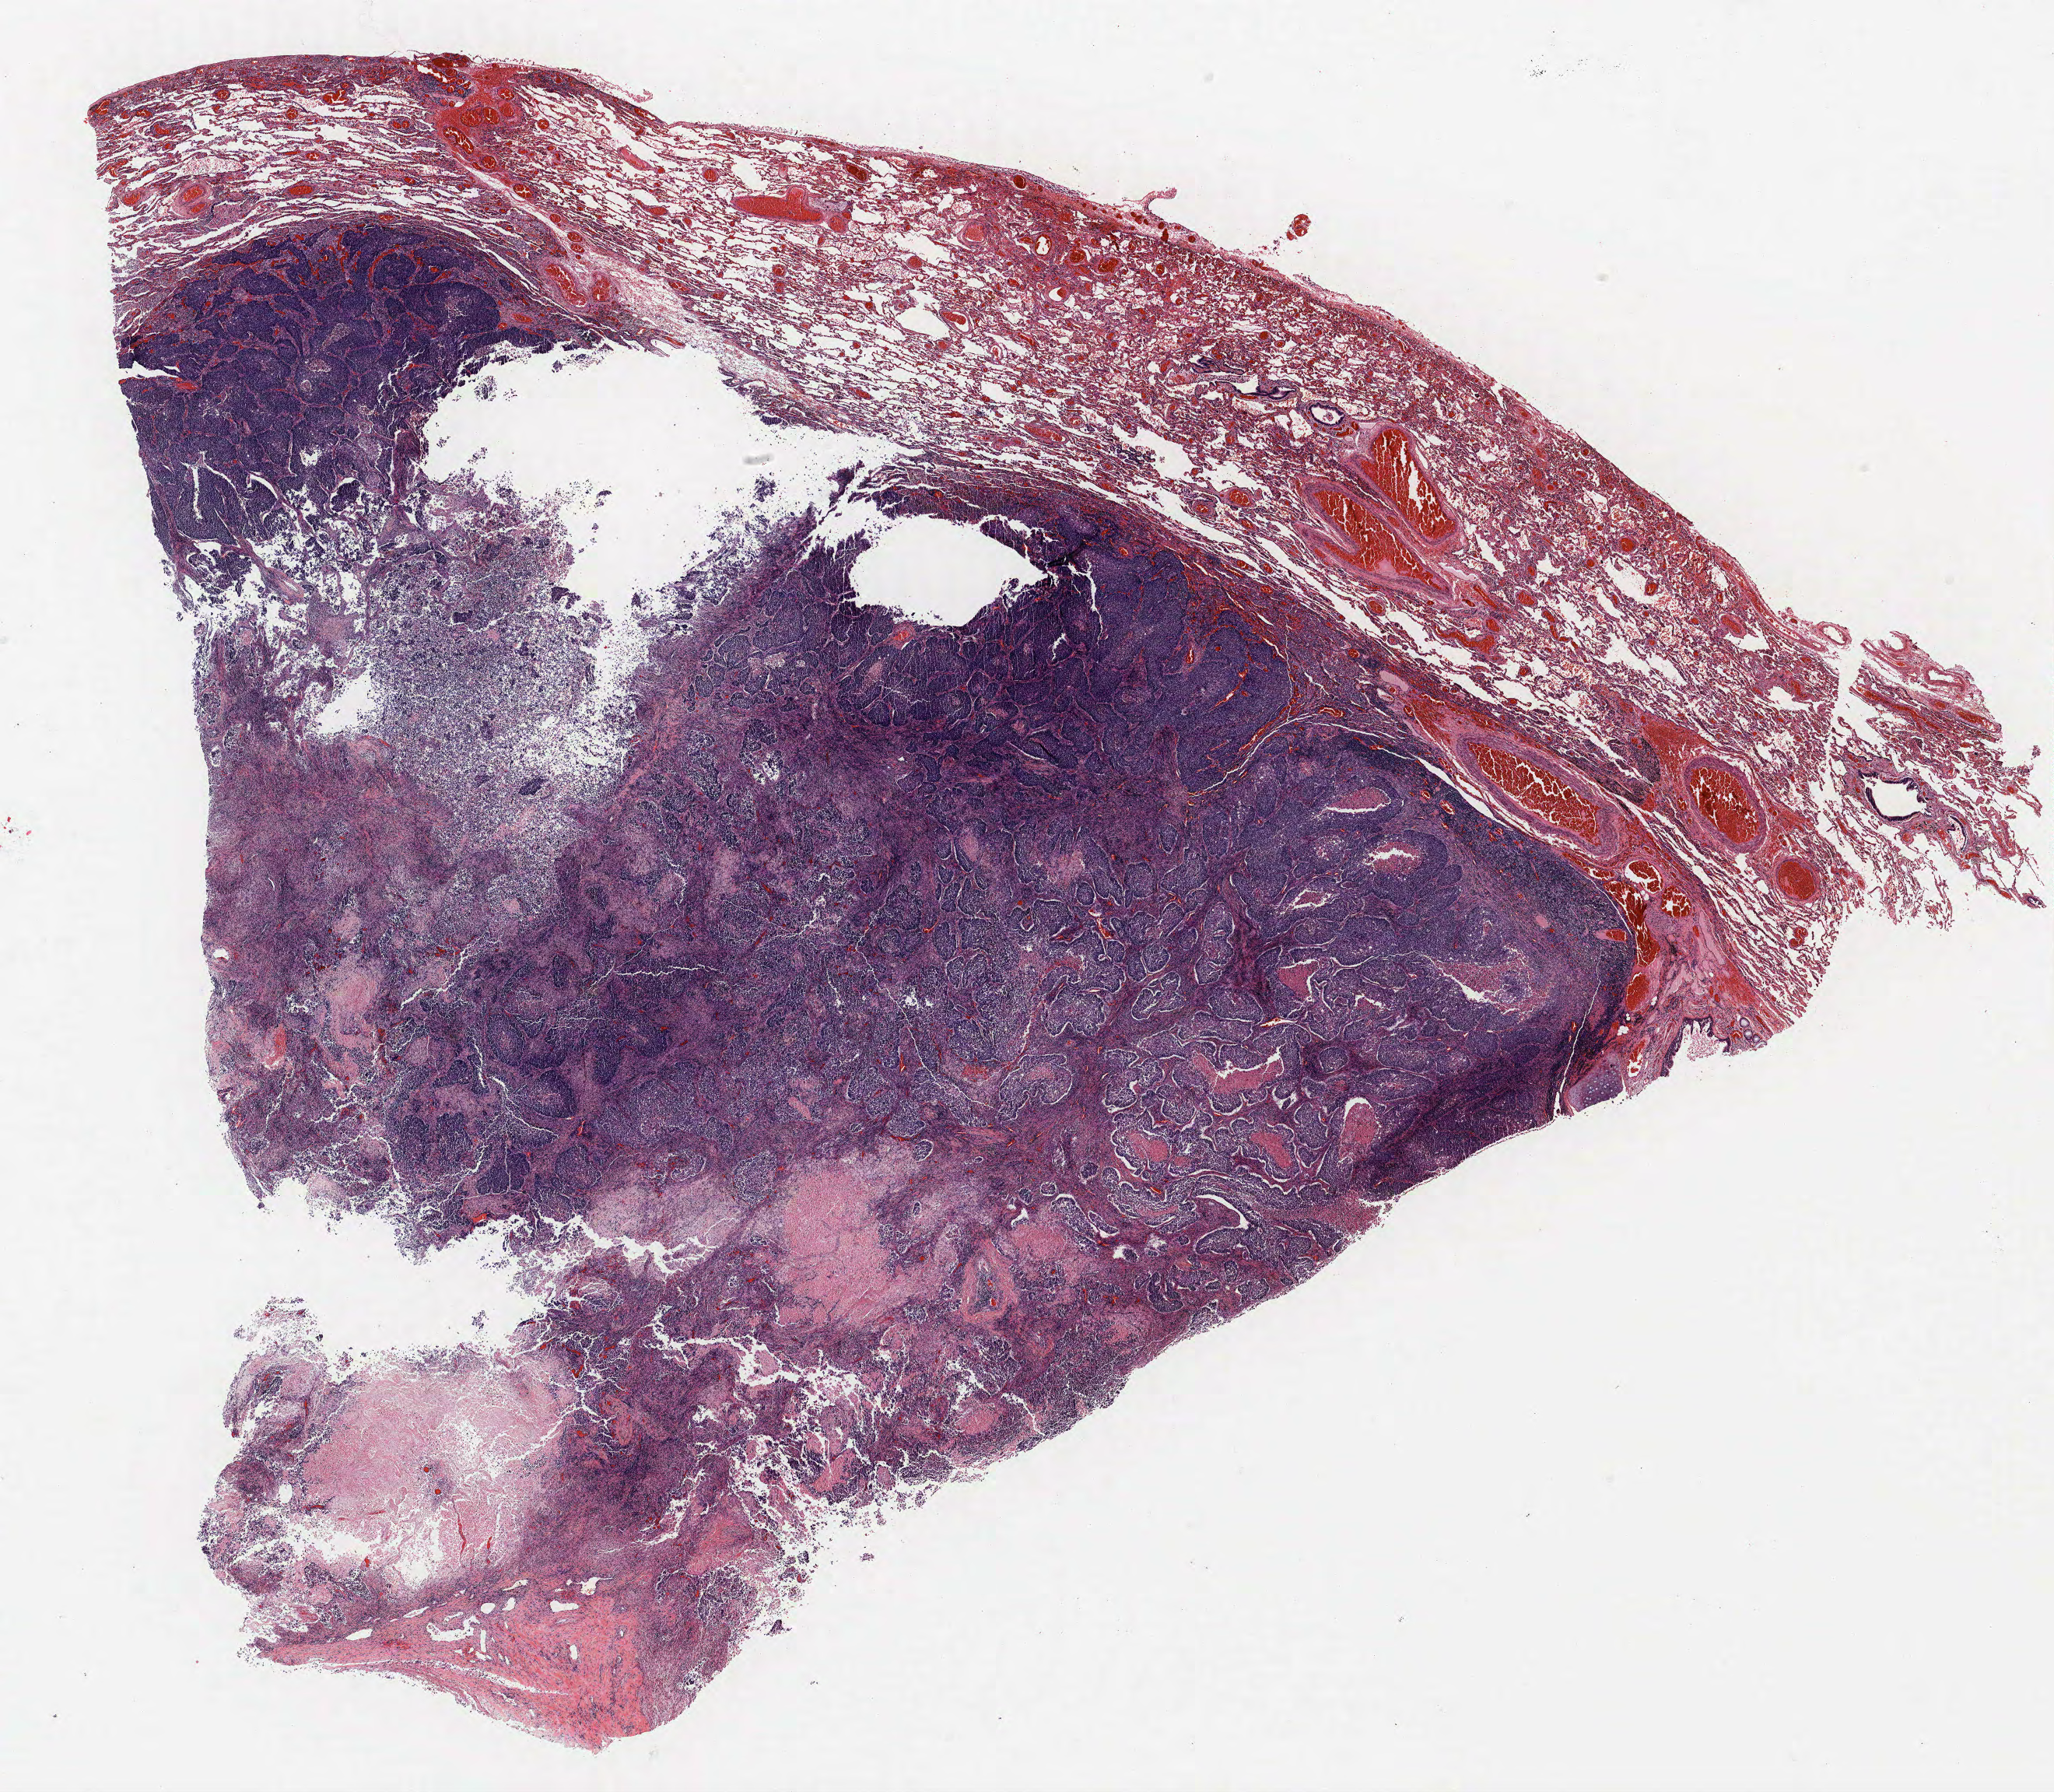
H&E whole-slide image, shown as a low-resolution overview of the whole scanned area (about 21.1 x 18.4 mm). Formalin-fixed paraffin-embedded (FFPE) section. Lung tissue. Male, age 69 at enrolment. Current smoker at enrolment. Grade: moderately differentiated (G2).
Tumour size (pathology): 40 mm. Stage (AJCC 6th edition): IB. Participant's lung-cancer diagnosis: Squamous cell carcinoma, NOS (ICD-O-3 8070/3). Primary tumour location (clinical record): right upper lobe.